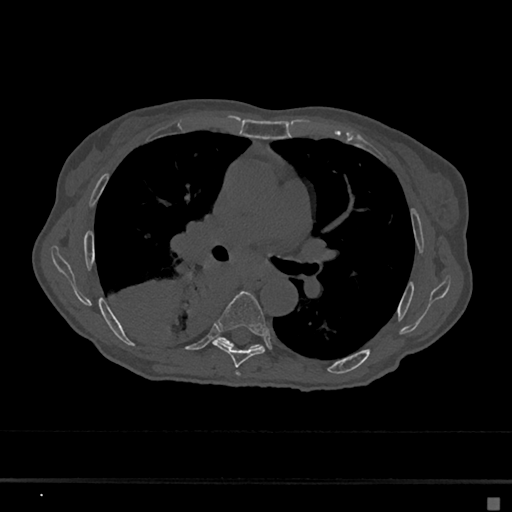
CT including the spine, one axial slice; slice 407 of 797 in the series (ordered by position); bone window (W 1800 / L 400 HU); 0.5 mm slice thickness; 512 × 512 image matrix, field of view 360 × 360 mm. Female patient, age 68 years. From the clinical record (not read from this slice): primary cancer: renal.
Structures marked on this image (semi-automatic segmentation, software-assisted and operator-edited):
- T5 vertebra: bounding box <235,371,240,376> (left, top, right, bottom; pixels)
- T6 vertebra: <213,291,268,368>
- T7 vertebra: <219,337,260,348>